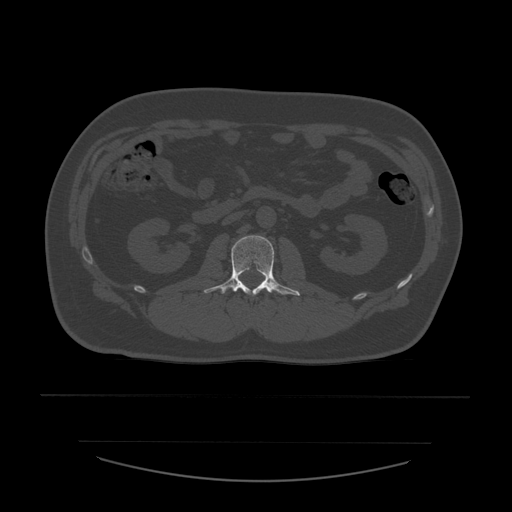
CT including the spine, one axial slice; reconstruction kernel STANDARD; bone window (W 1800 / L 400 HU); 1.25 mm slice thickness; 512 × 512 image matrix, field of view 441 × 441 mm. Patient age 44 years. Case-level facts recorded for this patient, not image findings: primary cancer: soft tissue sarcoma.
Structures marked on this image (semi-automatically segmented with operator editing):
- L2 vertebra: box from (x=204, y=235) to (x=301, y=296) px